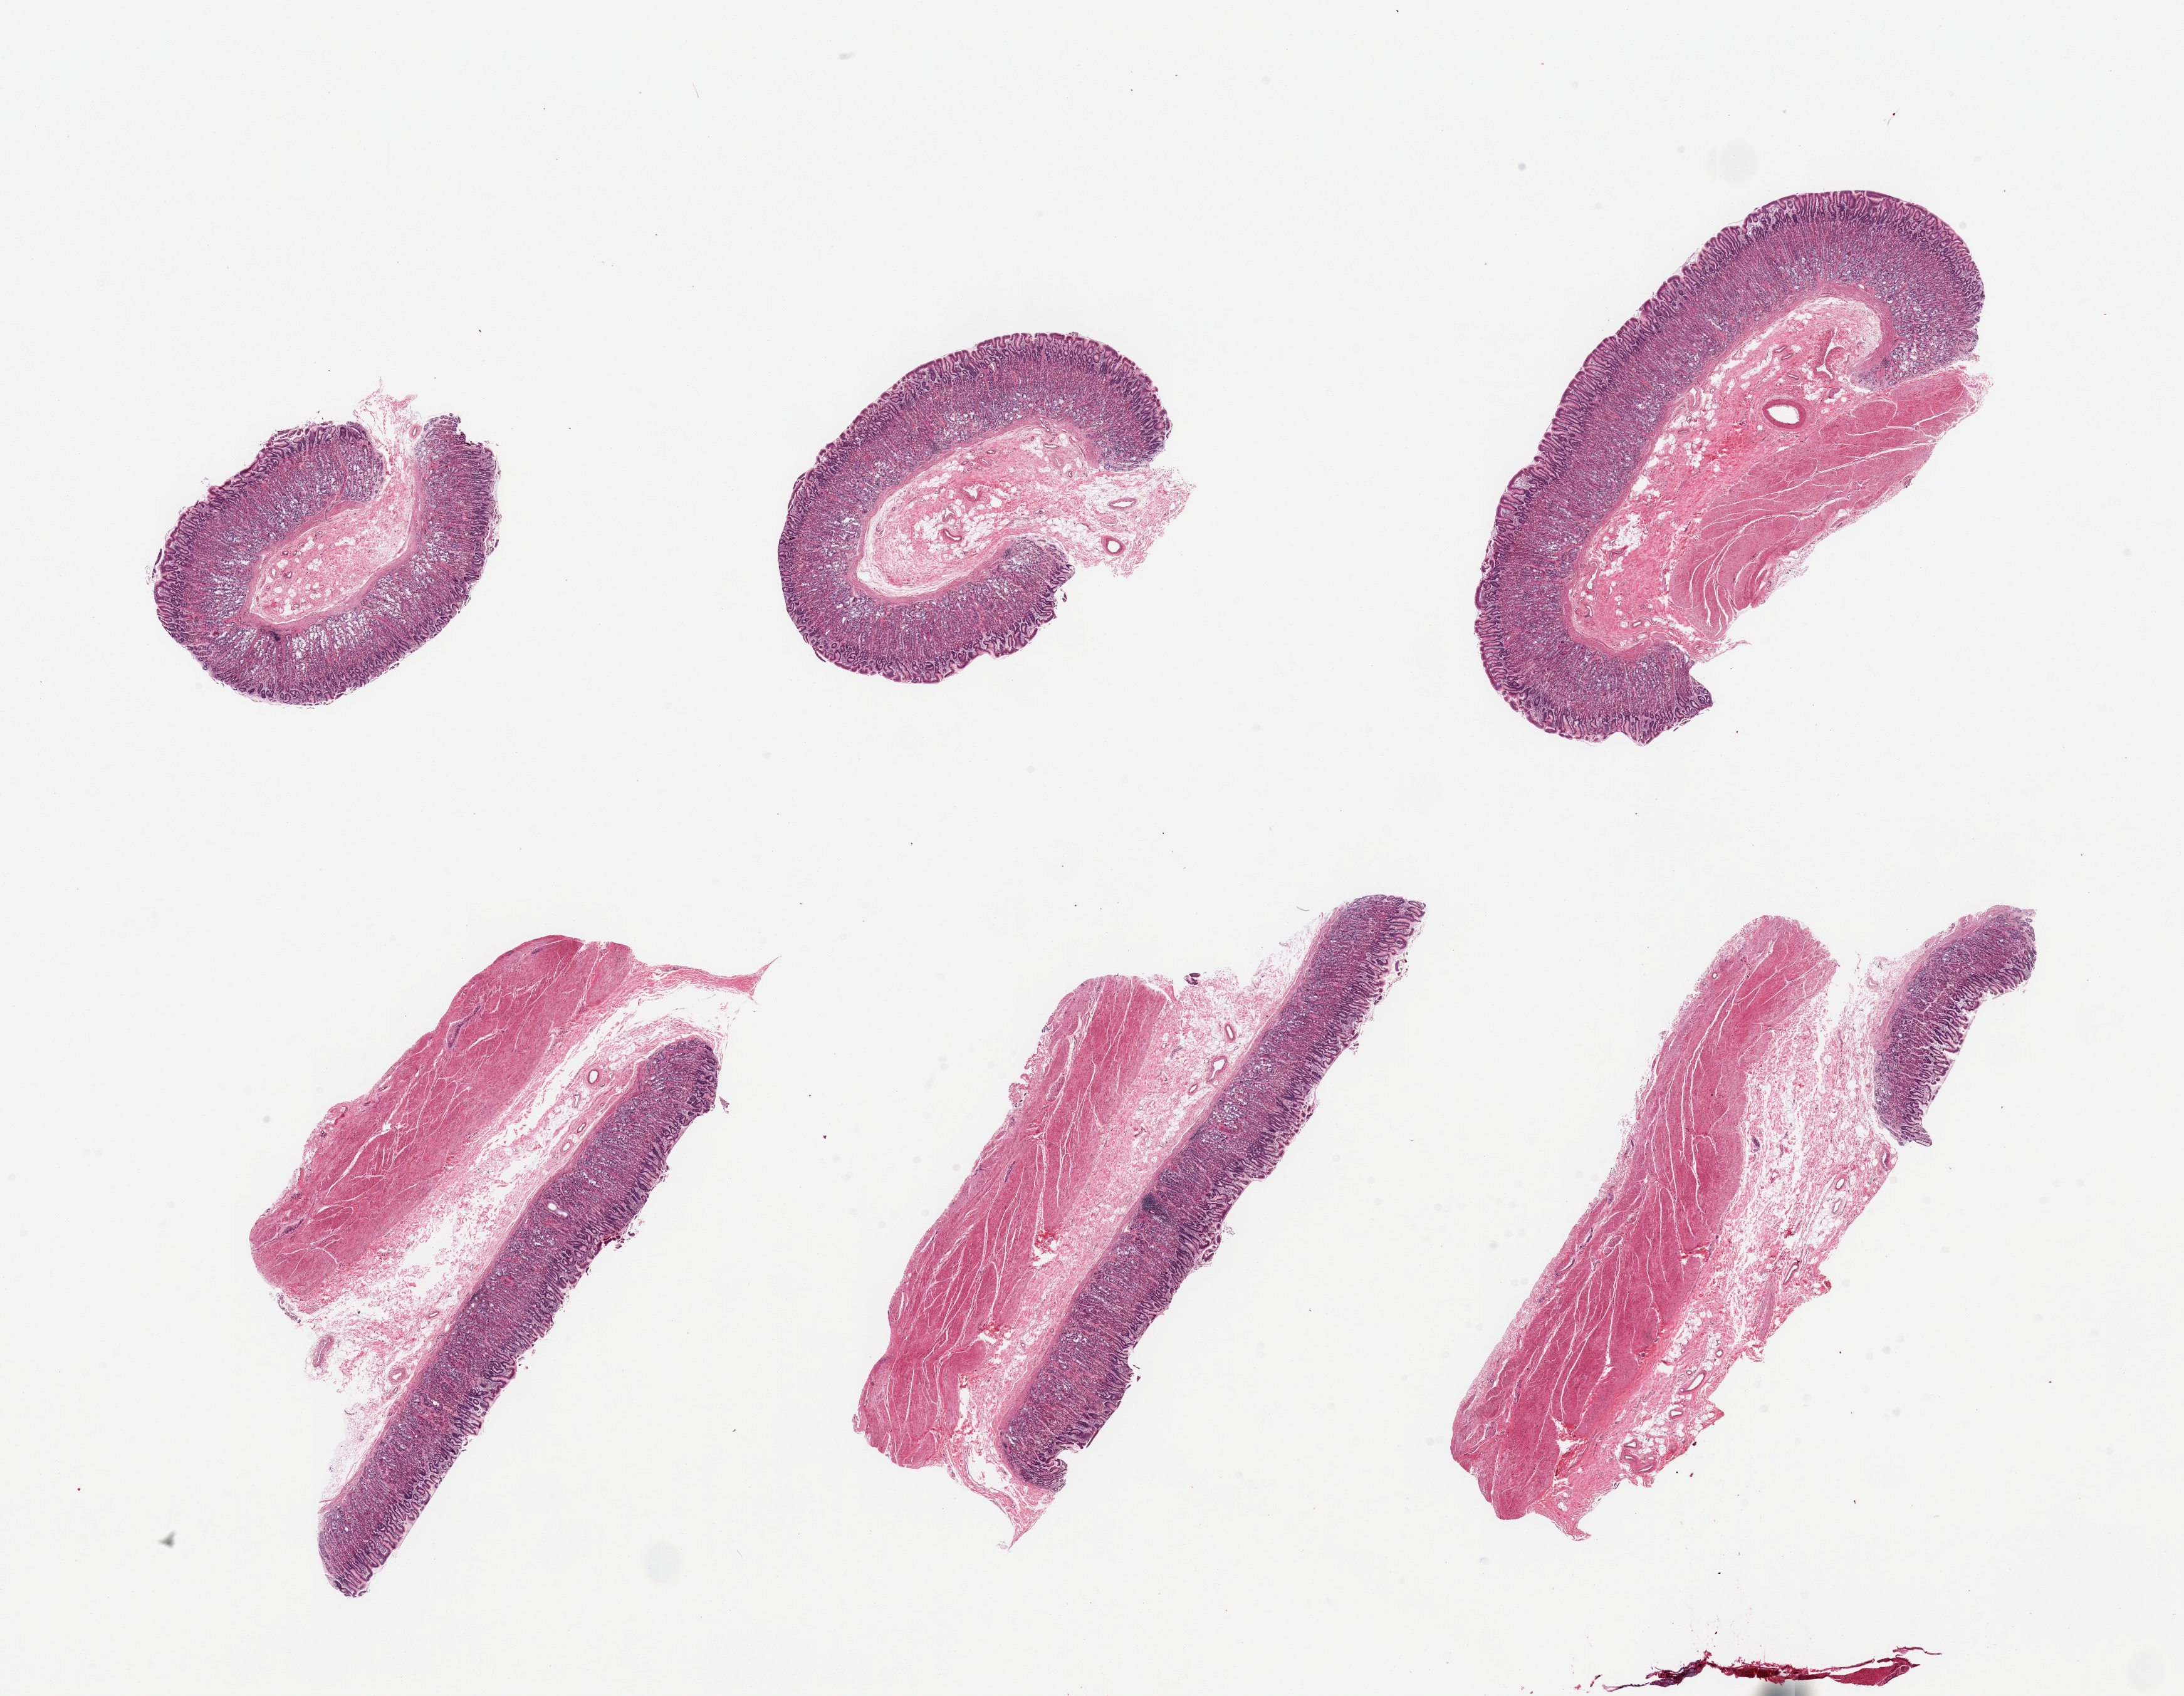
Haematoxylin and eosin whole-slide image, a low-resolution overview of the entire scanned area, about 27.6 x 21.4 mm (slide scanned at 20x); PAXgene-fixed, paraffin-embedded tissue; sampled site (target tissue): stomach; donor tissue sample.
Reviewer comment on this tissue sample: 6 pieces; 4 have full thickness wall, 2 are without muscularis.